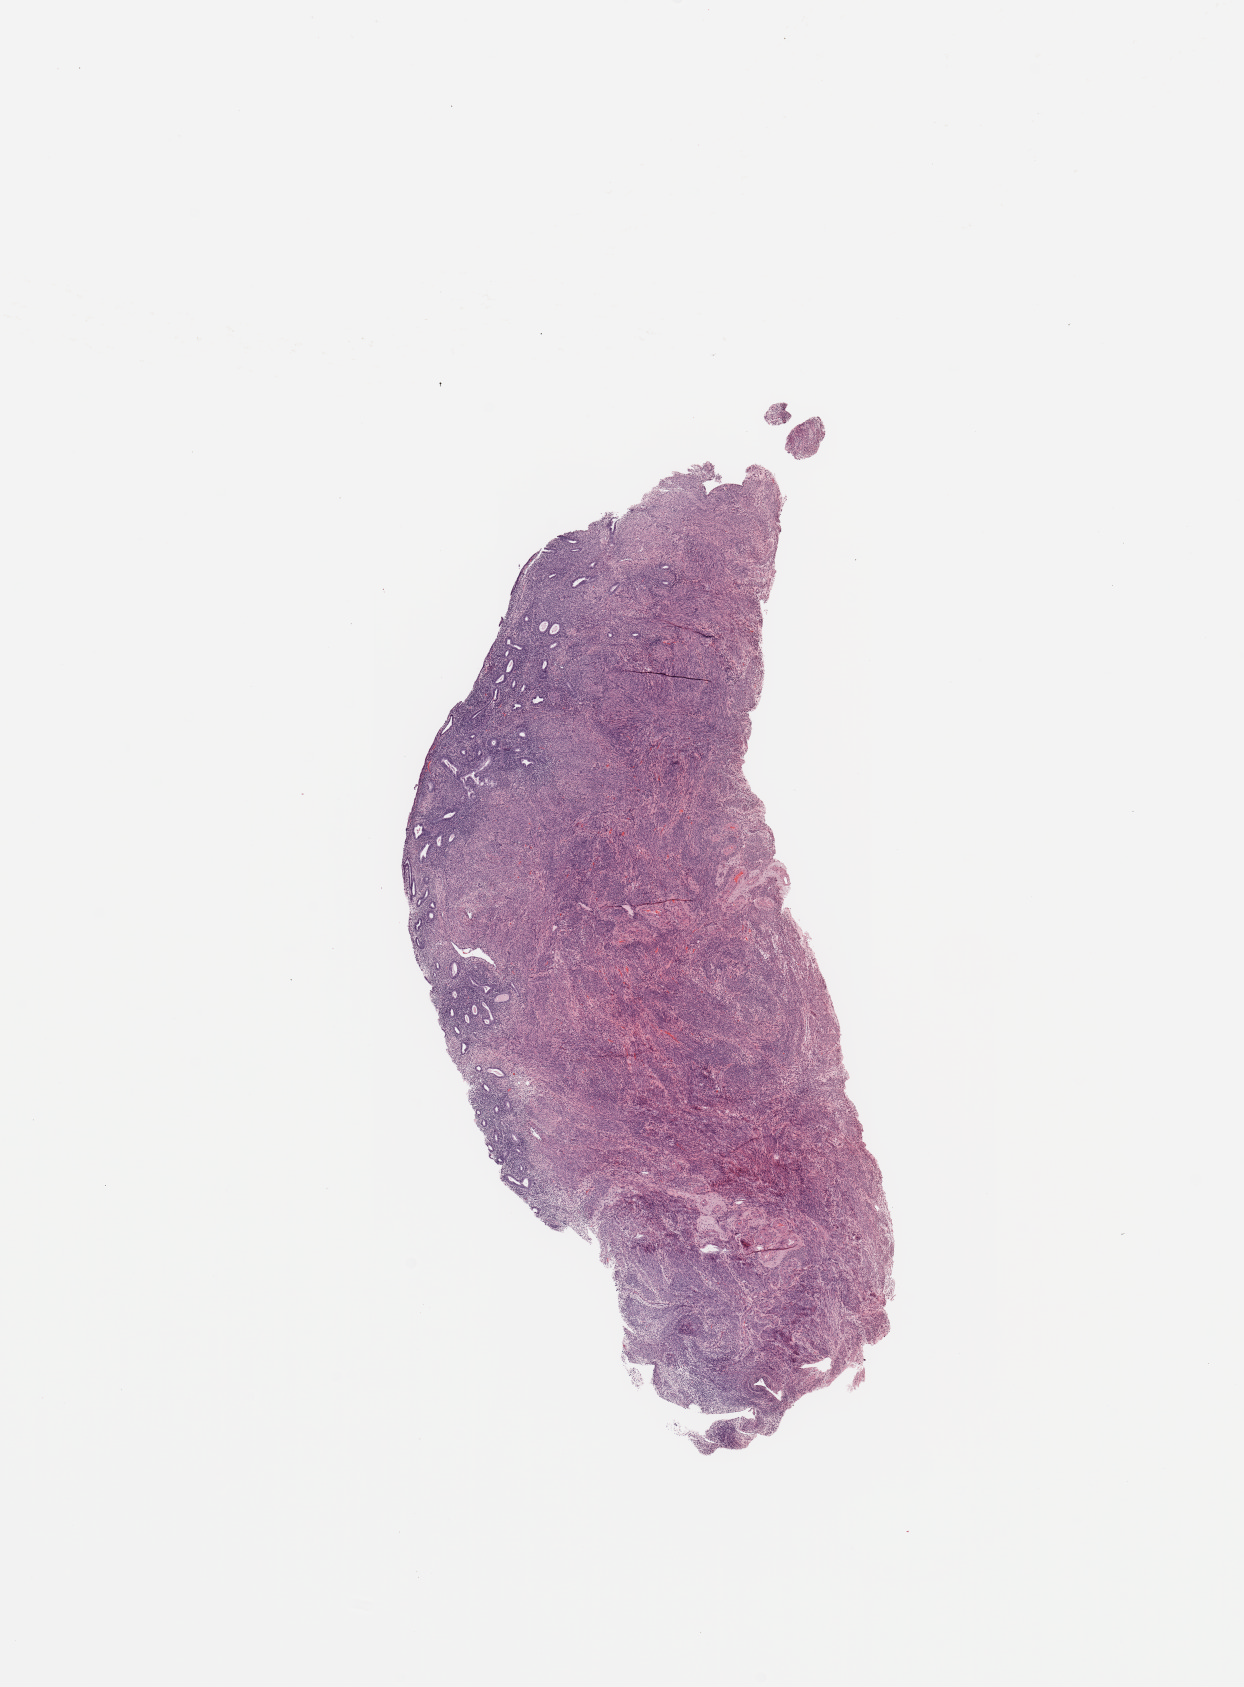
Whole-slide histology image, H&E-stained — low-resolution overview of the scanned area, about 9.8 x 13.3 mm (slide scanned at 20x); normal (non-tumour) tissue sample, uterus. 60-year-old female patient.
• this section: normal (non-tumour) tissue from the same patient
• patient diagnosis: Endometrioid adenocarcinoma, NOS